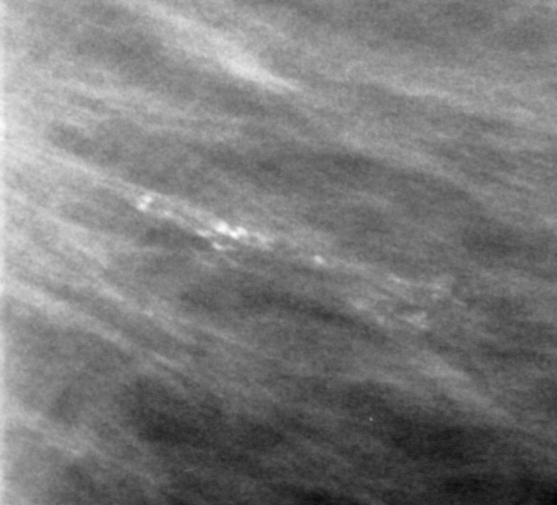
Crop from a digitized film mammogram around one marked abnormality, left breast, MLO view.
Calcifications, morphology pleomorphic, distribution segmental; BI-RADS assessment category 0; subtlety rating 4 on a 1 (subtle) to 5 (obvious) scale; pathology result (as recorded, not read from the image): benign.